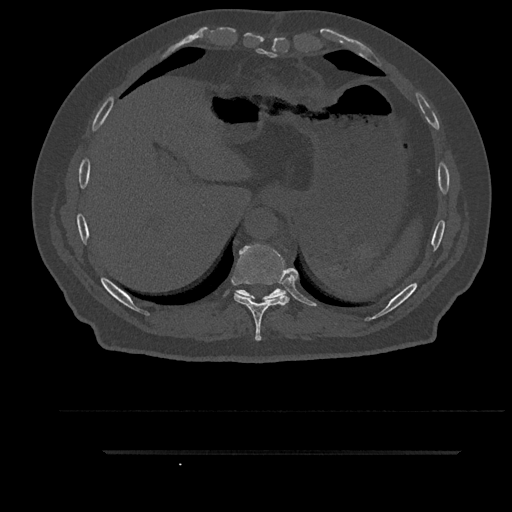
CT including the spine, one axial slice. Slice 405 of 797 in the series (ordered by position). 120 kVp. Bone window (W 1800 / L 400 HU). 0.5 mm slice thickness. 512 × 512 image matrix, field of view 432 × 432 mm. Male patient, age 63 years. Case-level facts recorded for this patient, not image findings: primary cancer: renal; vertebrae with lytic lesions (as recorded): T8.
Structures marked on this image (semi-automatic segmentation, software-assisted and operator-edited):
- T10 vertebra: bounding box (x1, y1, x2, y2) in pixels: (235, 289, 287, 300)
- T9 vertebra: (234, 244, 289, 341)